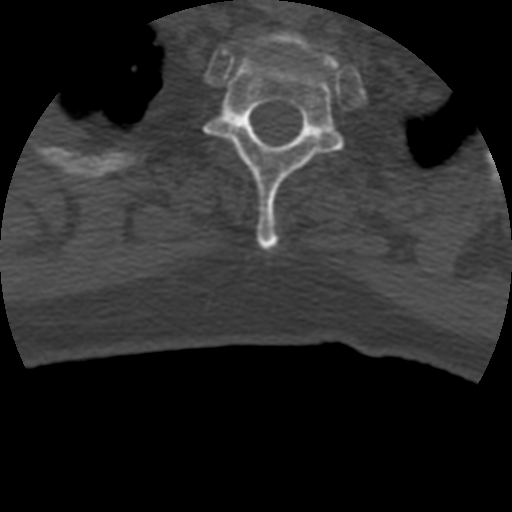
CT including the spine, one axial slice; position 368 of 399 along the scan axis; reconstruction kernel STANDARD; bone window (W 1800 / L 400 HU); 1.25 mm slice thickness; 512 × 512 image matrix, field of view 160 × 160 mm. Patient age 69 years. From the clinical record (not read from this slice): primary cancer: prostate.
Structures marked on this image (semi-automatic segmentation, software-assisted and operator-edited):
- T1 vertebra: bounding box <273,33,339,71> (left, top, right, bottom; pixels)
- T2 vertebra: <204,48,343,252>
- T3 vertebra: <352,174,366,192>